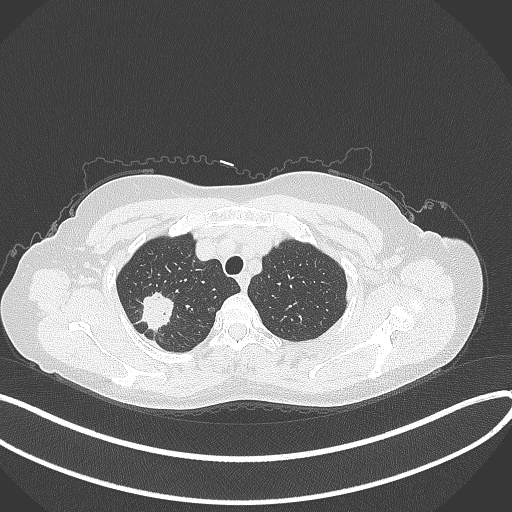
Chest CT, one axial slice. Position 307 of 337 along the scan axis. 120 kVp. Lung window (W 1500 / L -600 HU). 1 mm slice thickness. 512 × 512 image matrix. Patient: female, 50 years. From the clinical record (not read from this slice): clinical TNM (as recorded): T1c N0 M0.
Annotated regions visible in this slice (bounding box drawn by a radiologist):
- lung tumour (recorded histology: adenocarcinoma): bounding box [x1, y1, x2, y2] px = [133, 286, 176, 336]